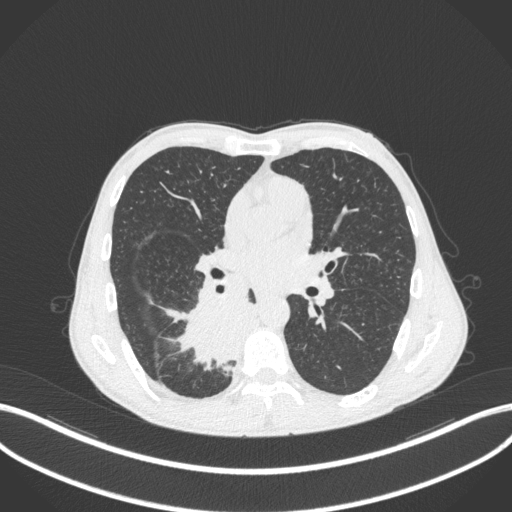
Chest CT, one axial slice; slice 195 of 371 in the series (ordered by position); lung window (W 1500 / L -600 HU); 512 × 512 image matrix, field of view 400 × 400 mm. Male patient, age 58 years. Case-level facts recorded for this patient, not image findings: clinical TNM (as recorded): T3 N1 M1.
Structures marked on this image (bounding box drawn by a radiologist):
- lung tumour (recorded histology: squamous cell carcinoma): bounding box (x1, y1, x2, y2) in pixels: (172, 292, 255, 368)